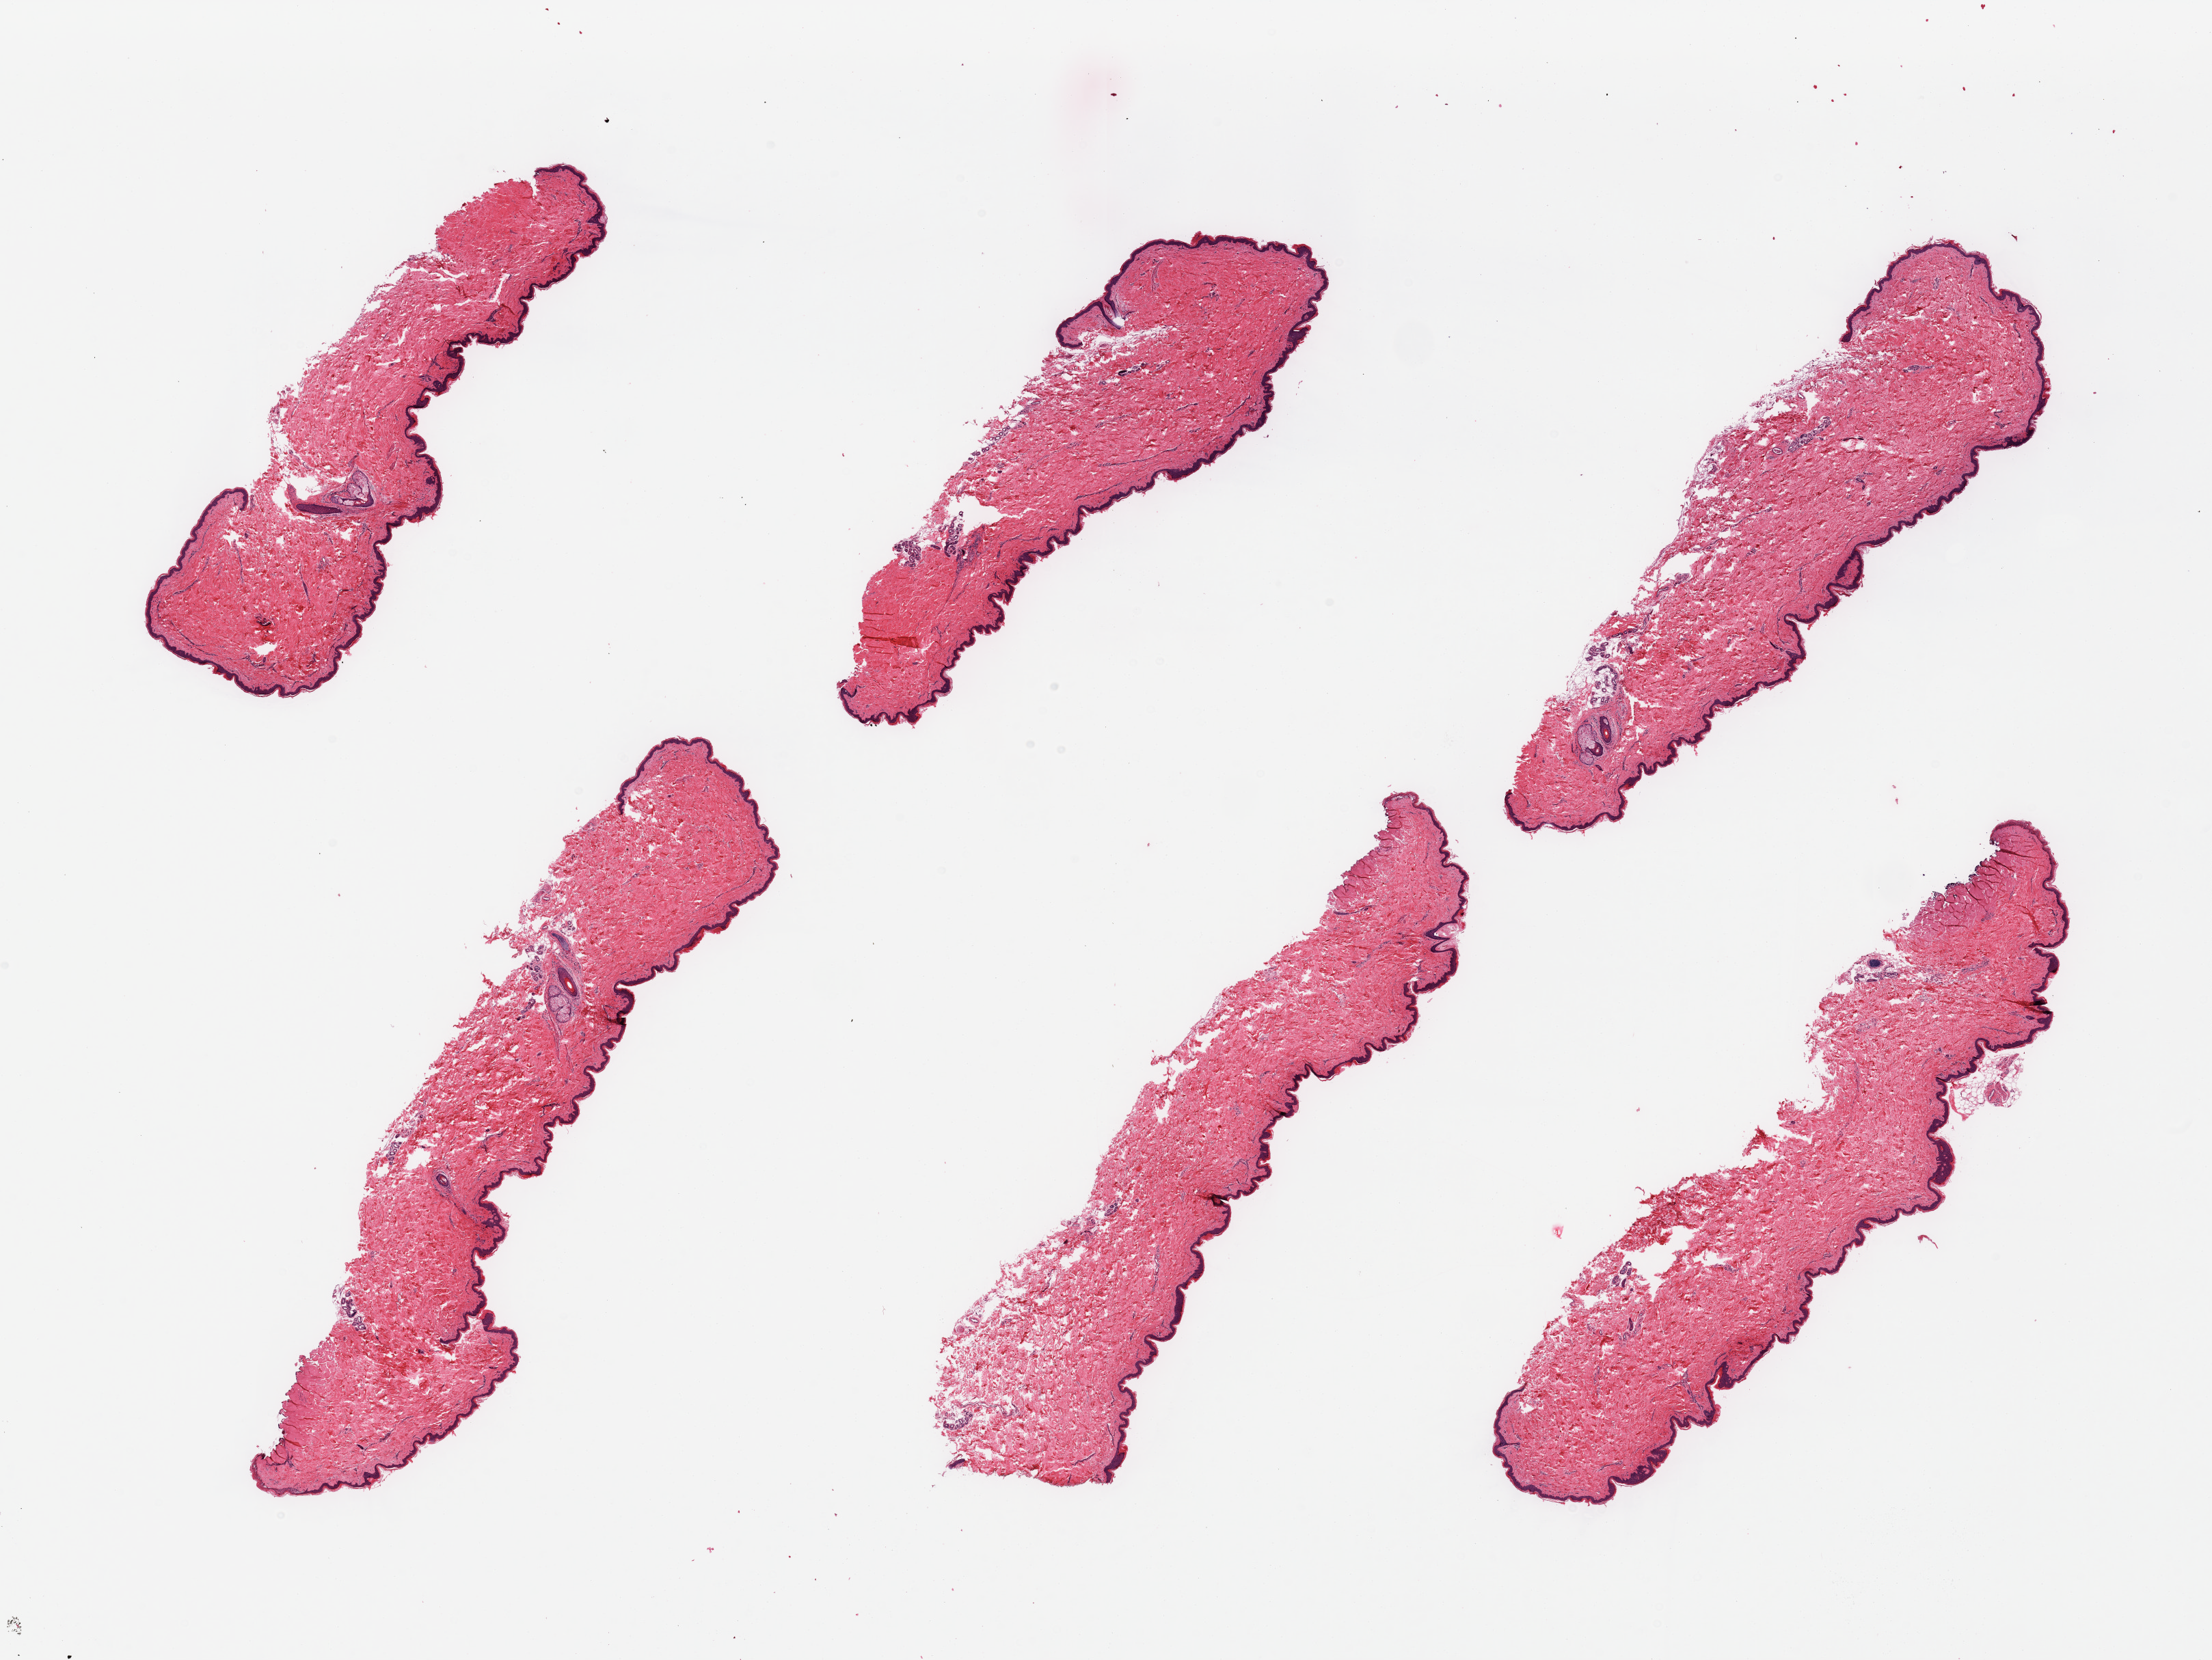
Whole-slide image, haematoxylin and eosin stain, whole scanned area (about 25.6 x 19.2 mm) shown as a low-resolution overview. PAXgene-fixed, paraffin-embedded tissue. Sampled site (target tissue): skin of suprapubic region. Tissue donor sample.
Review note (as recorded): 6 pieces, minimal dermal fat; squamous epithelium is ~50-60 microns.